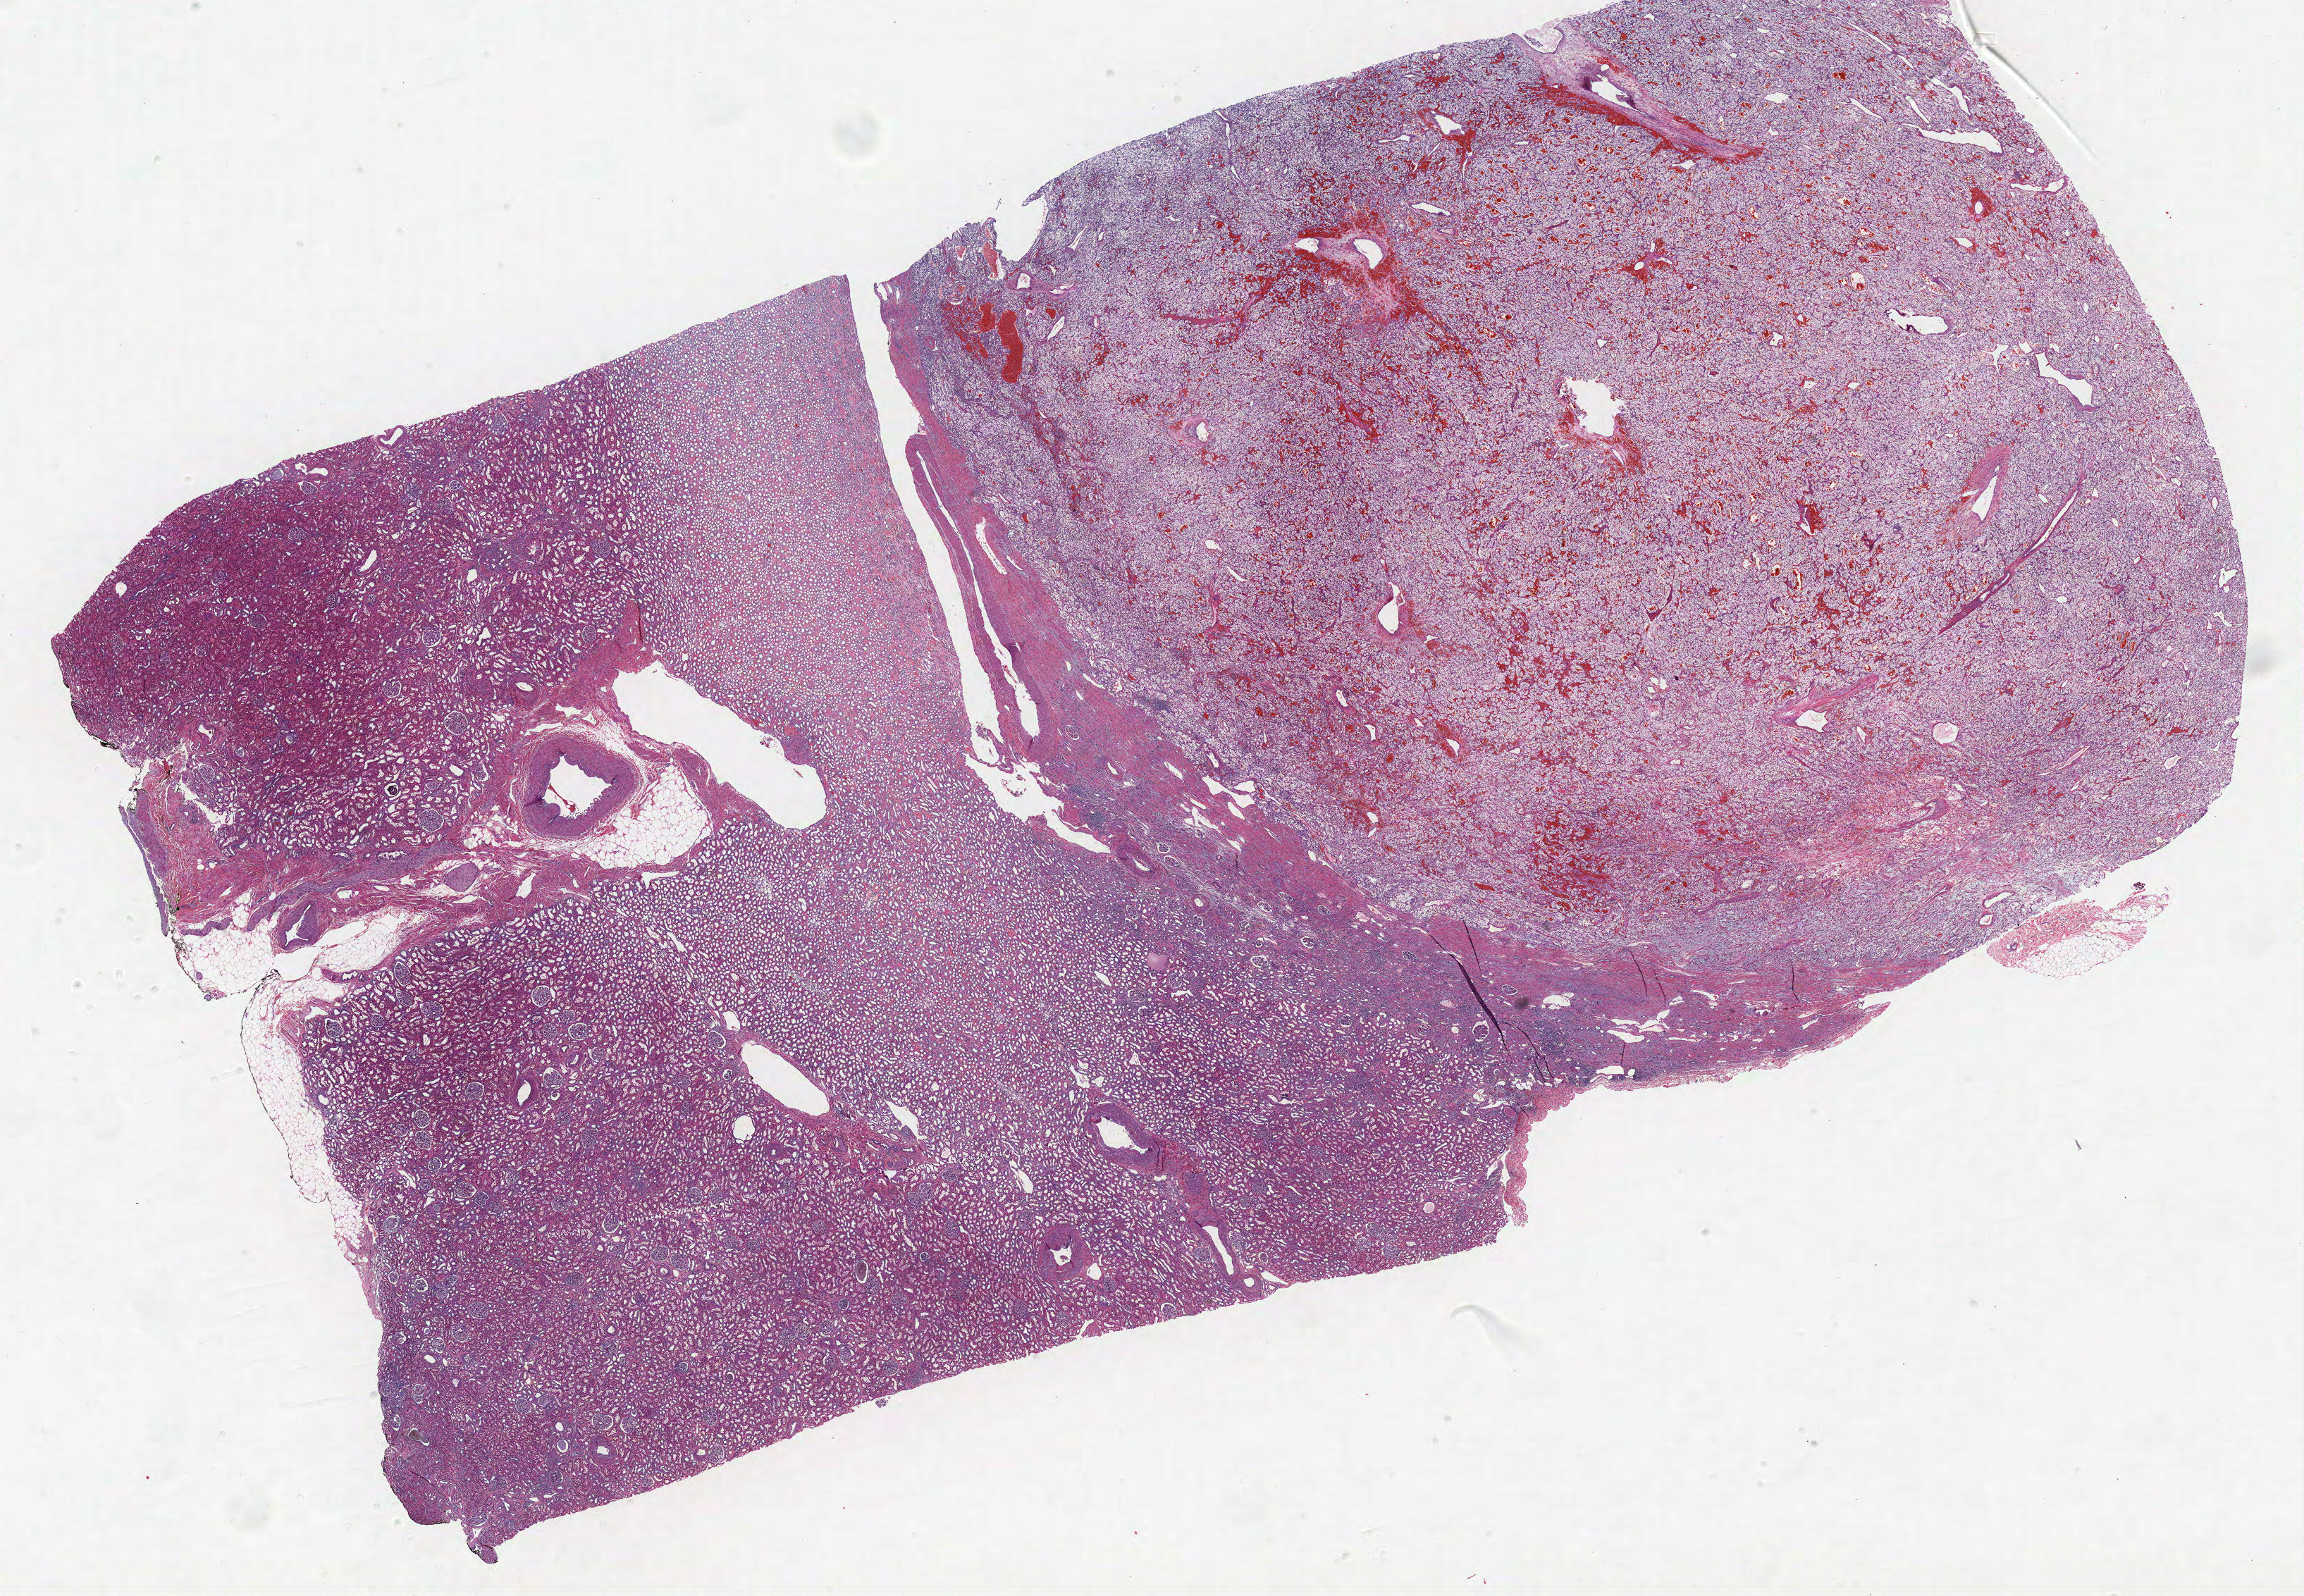
H&E whole-slide image, shown as a low-resolution overview of the whole scanned area (about 26.1 x 18.1 mm, acquisition: 40x scan). Formalin-fixed paraffin-embedded (FFPE) diagnostic section. Kidney, primary tumour sample. Male, age 75 years at initial diagnosis. Histologic grade: G2 (moderately differentiated).
AJCC pathologic stage: I. Diagnosis: Clear cell adenocarcinoma, NOS. Laterality: left.